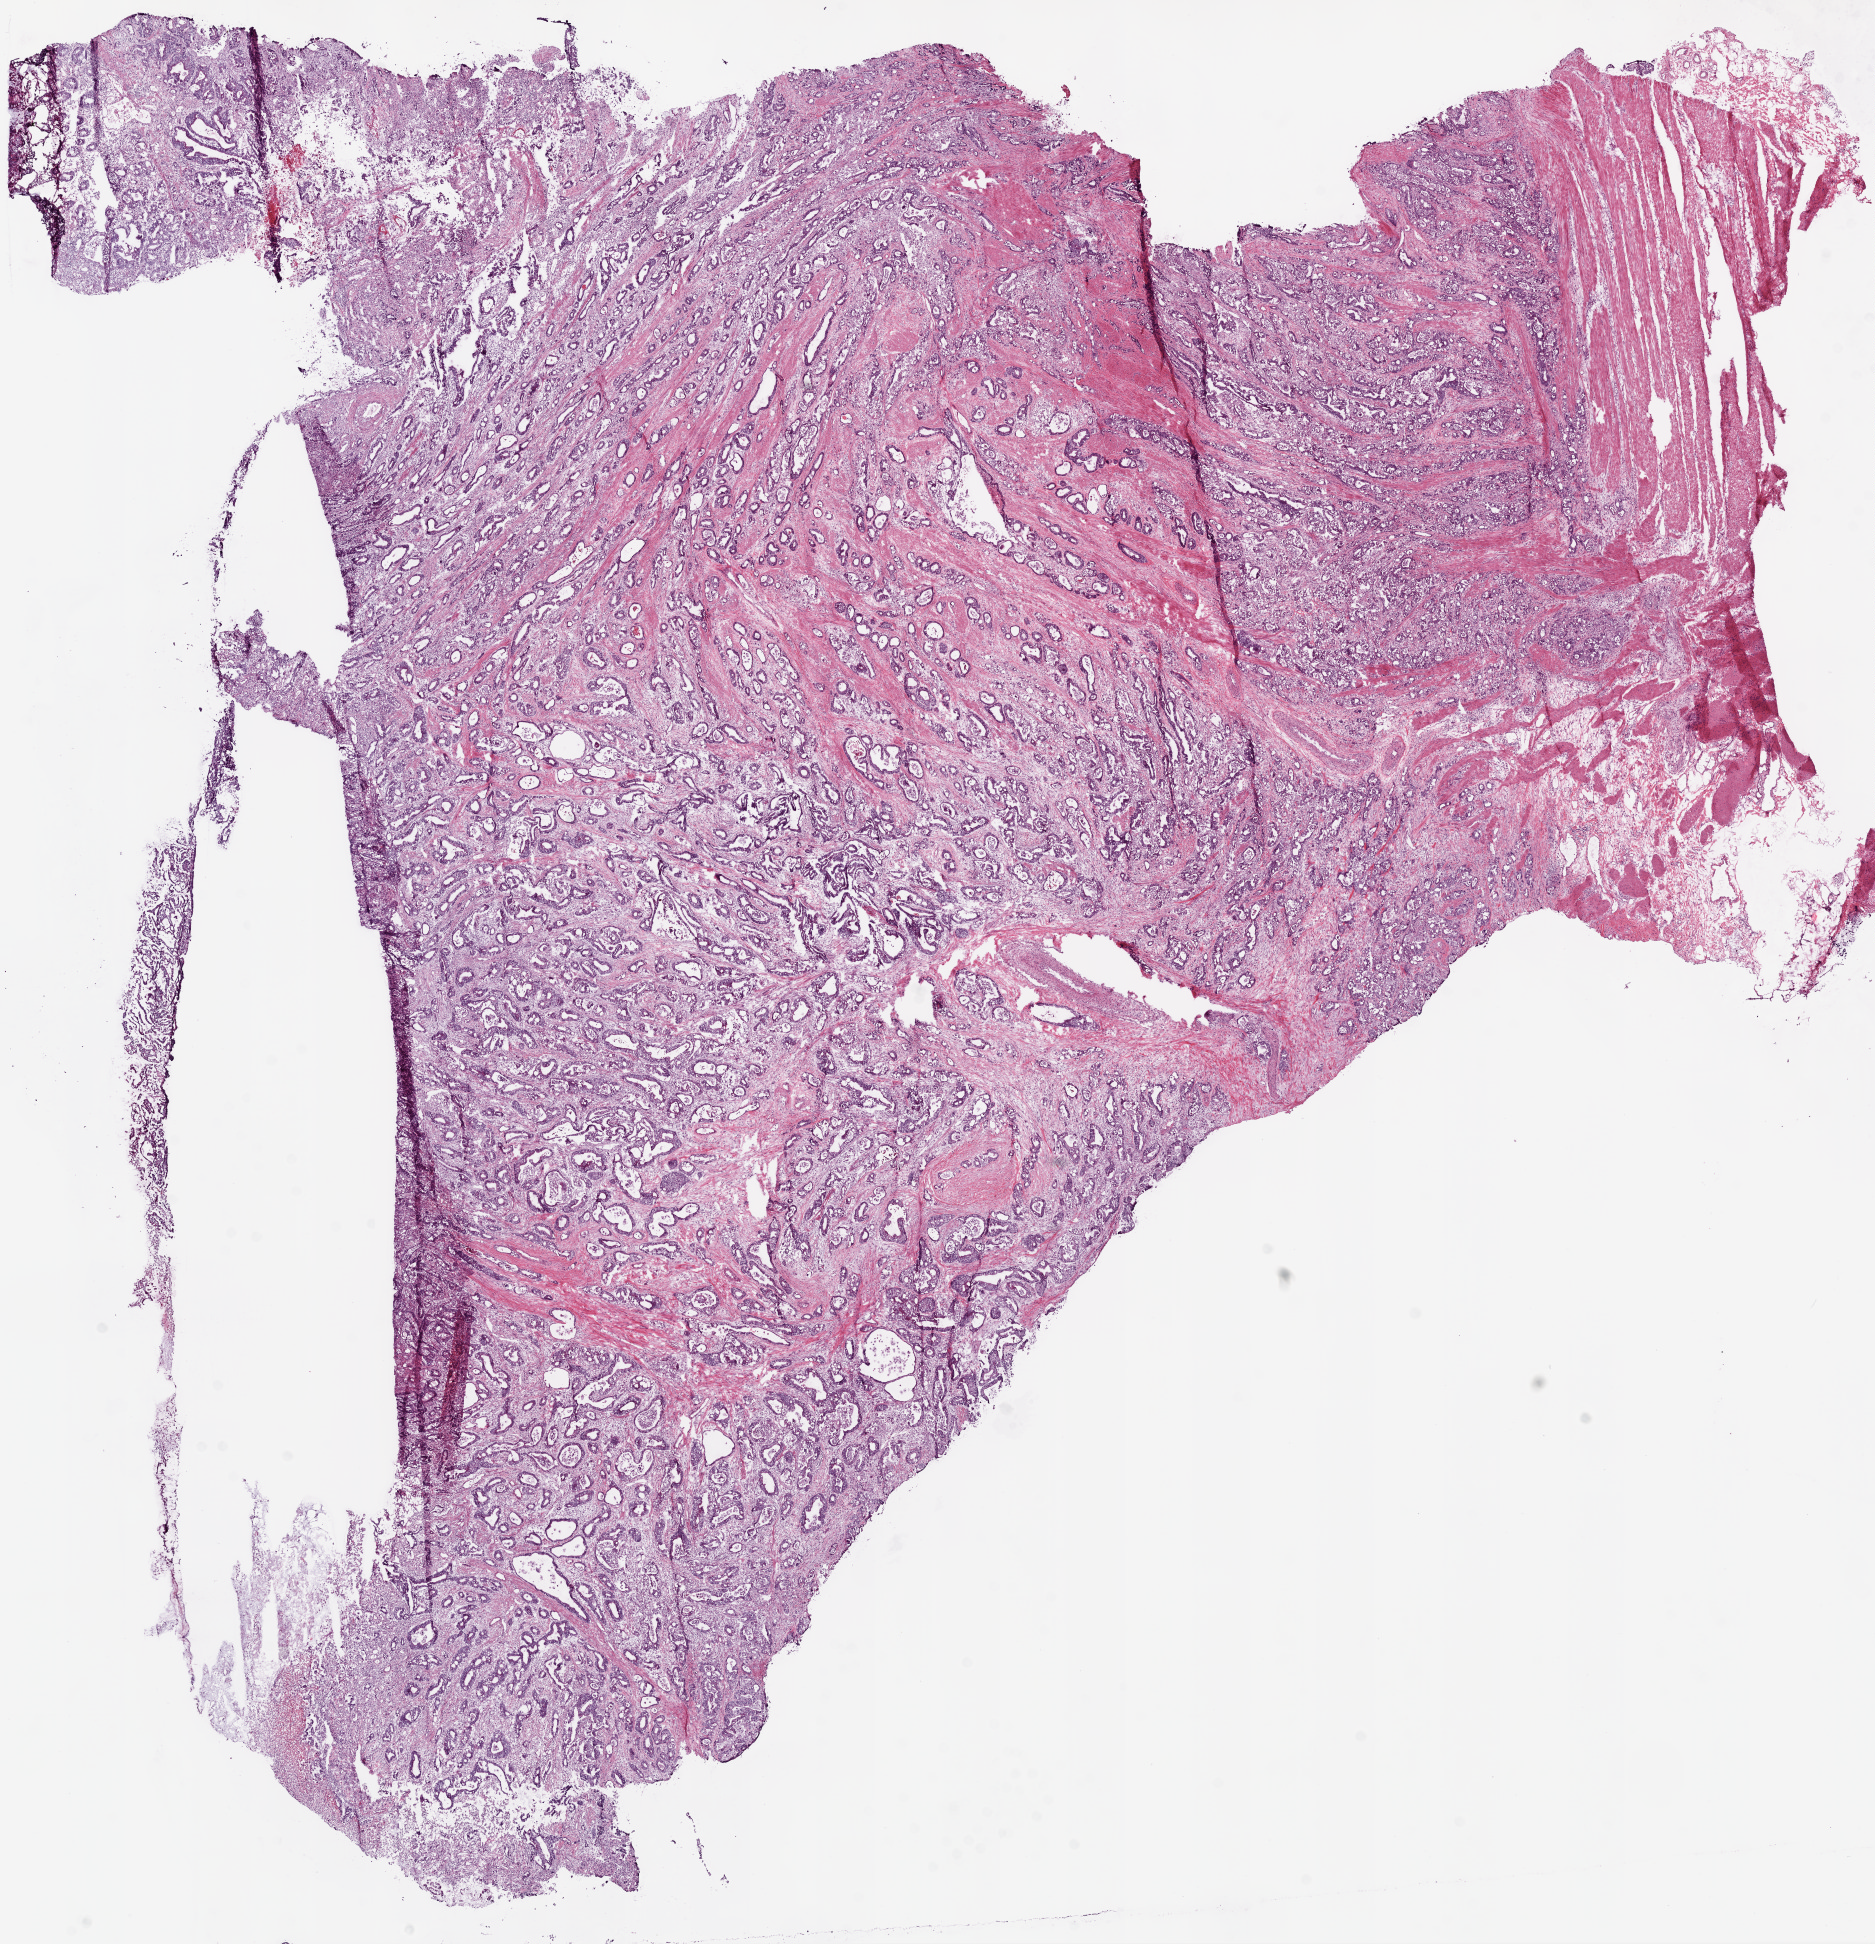
Whole-slide histology image, H&E, shown as a low-resolution overview of the whole scanned area (about 15.0 x 15.6 mm, acquisition: 20x scan). Frozen section from the bottom of the tissue portion. Primary tumour sample from the colon. Male patient; age at initial diagnosis 72 years. Slide review estimates, as recorded: tumour cells 88%, tumour nuclei 70%, normal cells 0%, stromal cells 10%, necrosis 2%. Infiltration values recorded for this section: lymphocyte infiltration 10%, monocyte infiltration 10%, neutrophil infiltration 2%.
* lymph nodes positive (case pathology): 1 of 19 examined
* AJCC pathologic stage: IIIB (7th edition)
* pathologic diagnosis: Adenocarcinoma, NOS